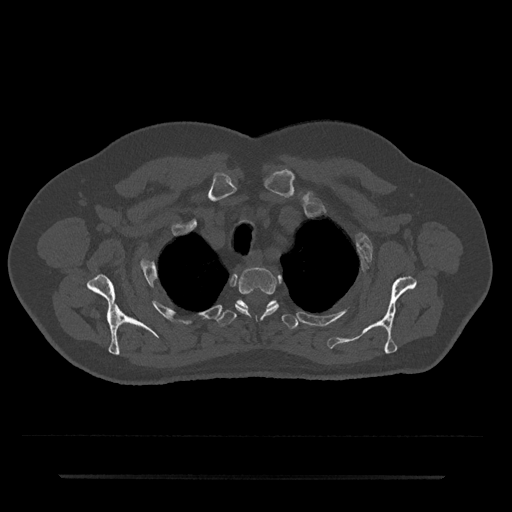
CT including the spine, one axial slice; slice 592 of 797 in the series (ordered by position); 120 kVp; bone window (W 1800 / L 400 HU); 512 × 512 image matrix, field of view 437 × 437 mm. Male patient, age 69 years. From the clinical record (not read from this slice): primary cancer: prostate.
Structures marked on this image (semi-automatic segmentation, software-assisted and operator-edited):
- T2 vertebra: bounding box [x1, y1, x2, y2] px = [235, 267, 279, 316]
- T3 vertebra: [217, 300, 298, 329]